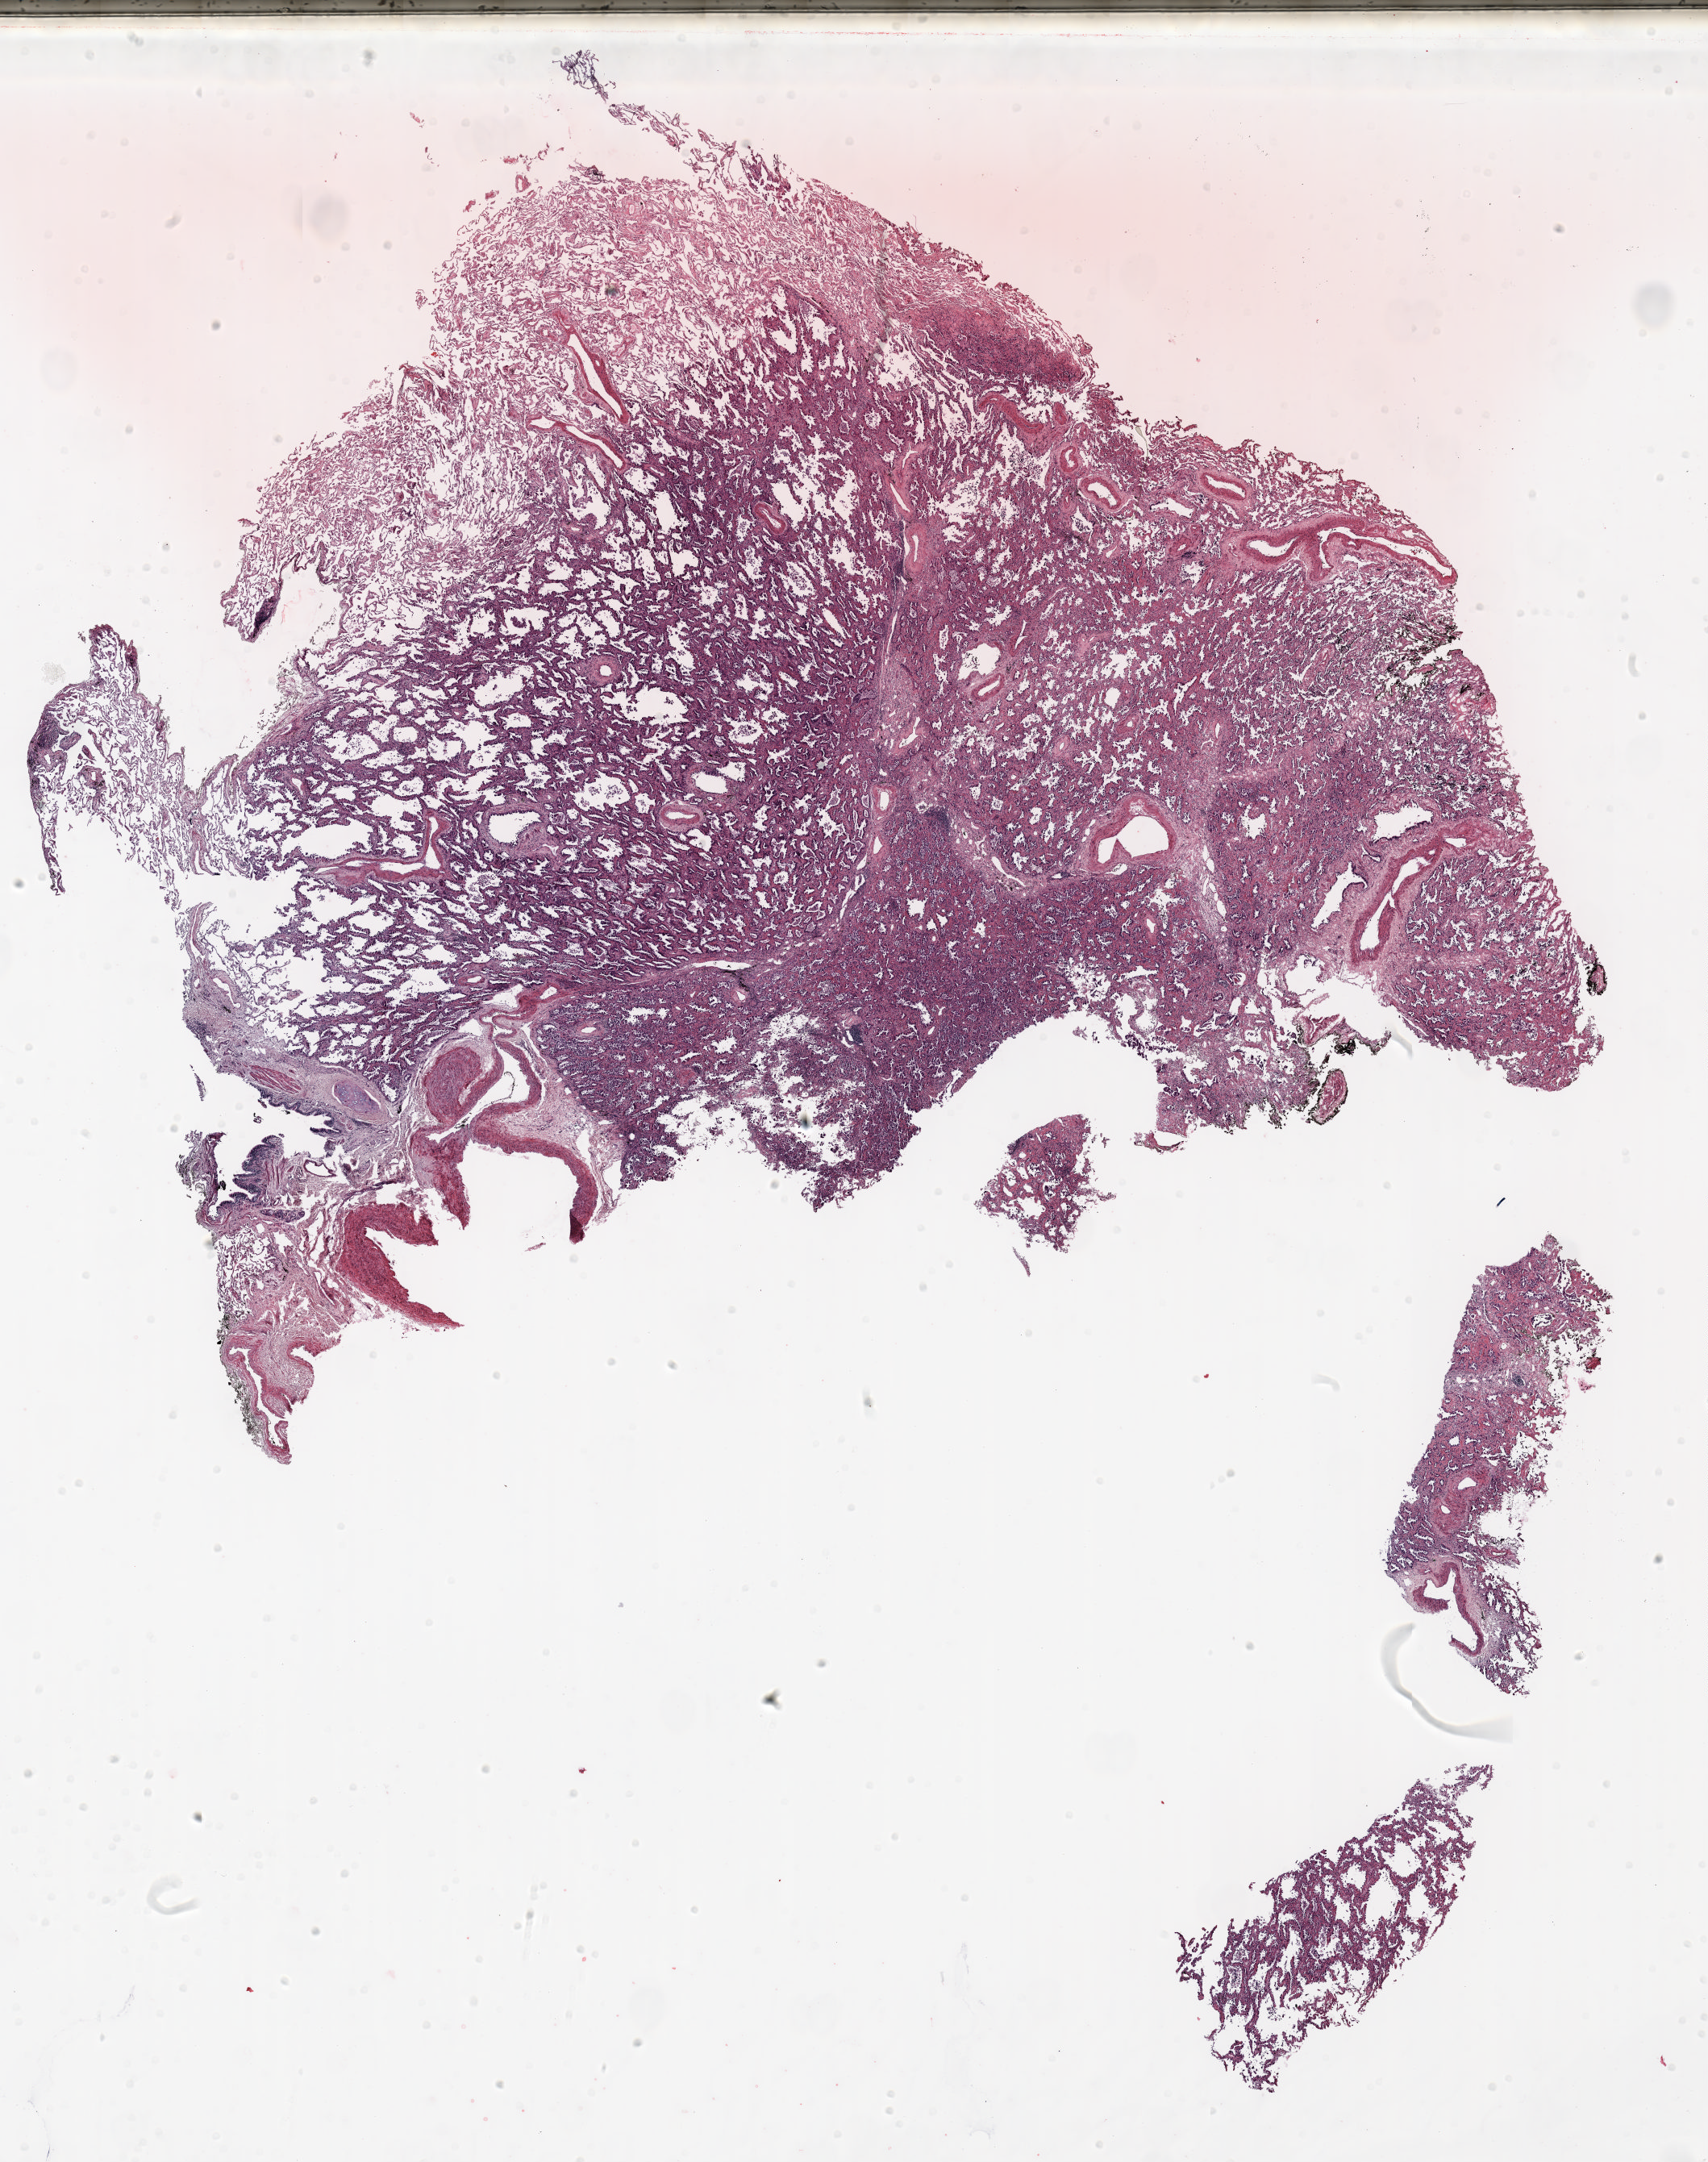
H&E-stained whole-slide image, low-resolution overview of the scanned area, about 17.0 x 21.5 mm, FFPE section, lung. Male, age 63 at enrolment. Former smoker at enrolment. Grade: moderately differentiated (G2).
Stage (AJCC 6th edition): IA. Tumour size (pathology): 14 mm. Primary tumour location (clinical record): left upper lobe. Participant's lung-cancer diagnosis: Adenocarcinoma, NOS.